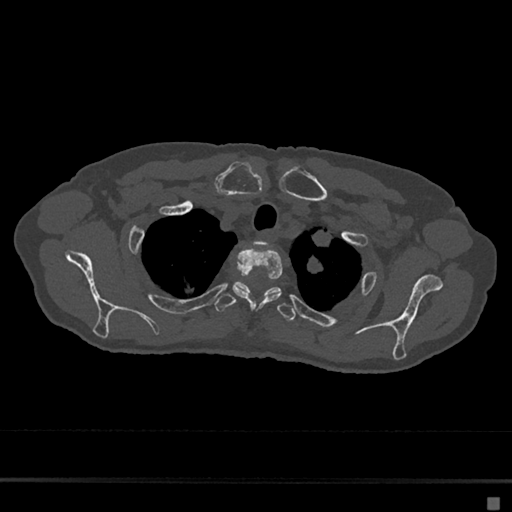
CT including the spine, one axial slice; position 564 of 797 along the scan axis; reconstruction kernel Br40s/3; bone window (W 1800 / L 400 HU); 512 × 512 image matrix, field of view 360 × 360 mm. Female patient, age 68 years. From the clinical record (not read from this slice): primary cancer: renal.
Outlined on this slice (semi-automatic segmentation, software-assisted and operator-edited):
- T1 vertebra: bounding box (x1, y1, x2, y2) in pixels: (256, 241, 268, 247)
- T2 vertebra: (232, 247, 283, 309)
- T3 vertebra: (214, 281, 296, 322)